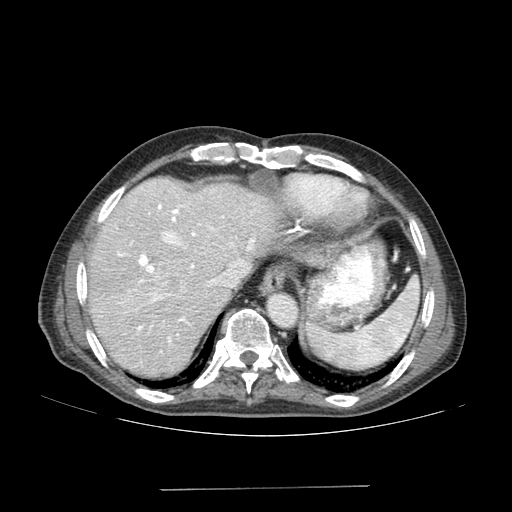
Contrast-enhanced abdominal CT (liver protocol), one axial slice. Position 136 of 192 along the scan axis. Reconstruction kernel SOFT. 120 kVp. Soft-tissue window (W 400 / L 40 HU). 2.5 mm slice thickness. 512 × 512 image matrix, field of view 400 × 400 mm. From the clinical record (not read from this slice): diagnosis: hepatocellular carcinoma (patient treated with transarterial chemoembolisation; whether this scan precedes or follows treatment is not stated here); TNM stage (as recorded): Stage-IVA; Child-Pugh class: A; tumour nodularity: uninodular.
Outlined on this slice (semi-automatic segmentation, software-assisted and operator-edited):
- liver parenchyma outside the tumour (the mass and vessels are separate outlines, so this box may not span the whole liver): box from (x=88, y=178) to (x=278, y=376) px
- mass: (x=130, y=270)–(x=173, y=307)
- liver vessels: (x=117, y=205)–(x=255, y=342)